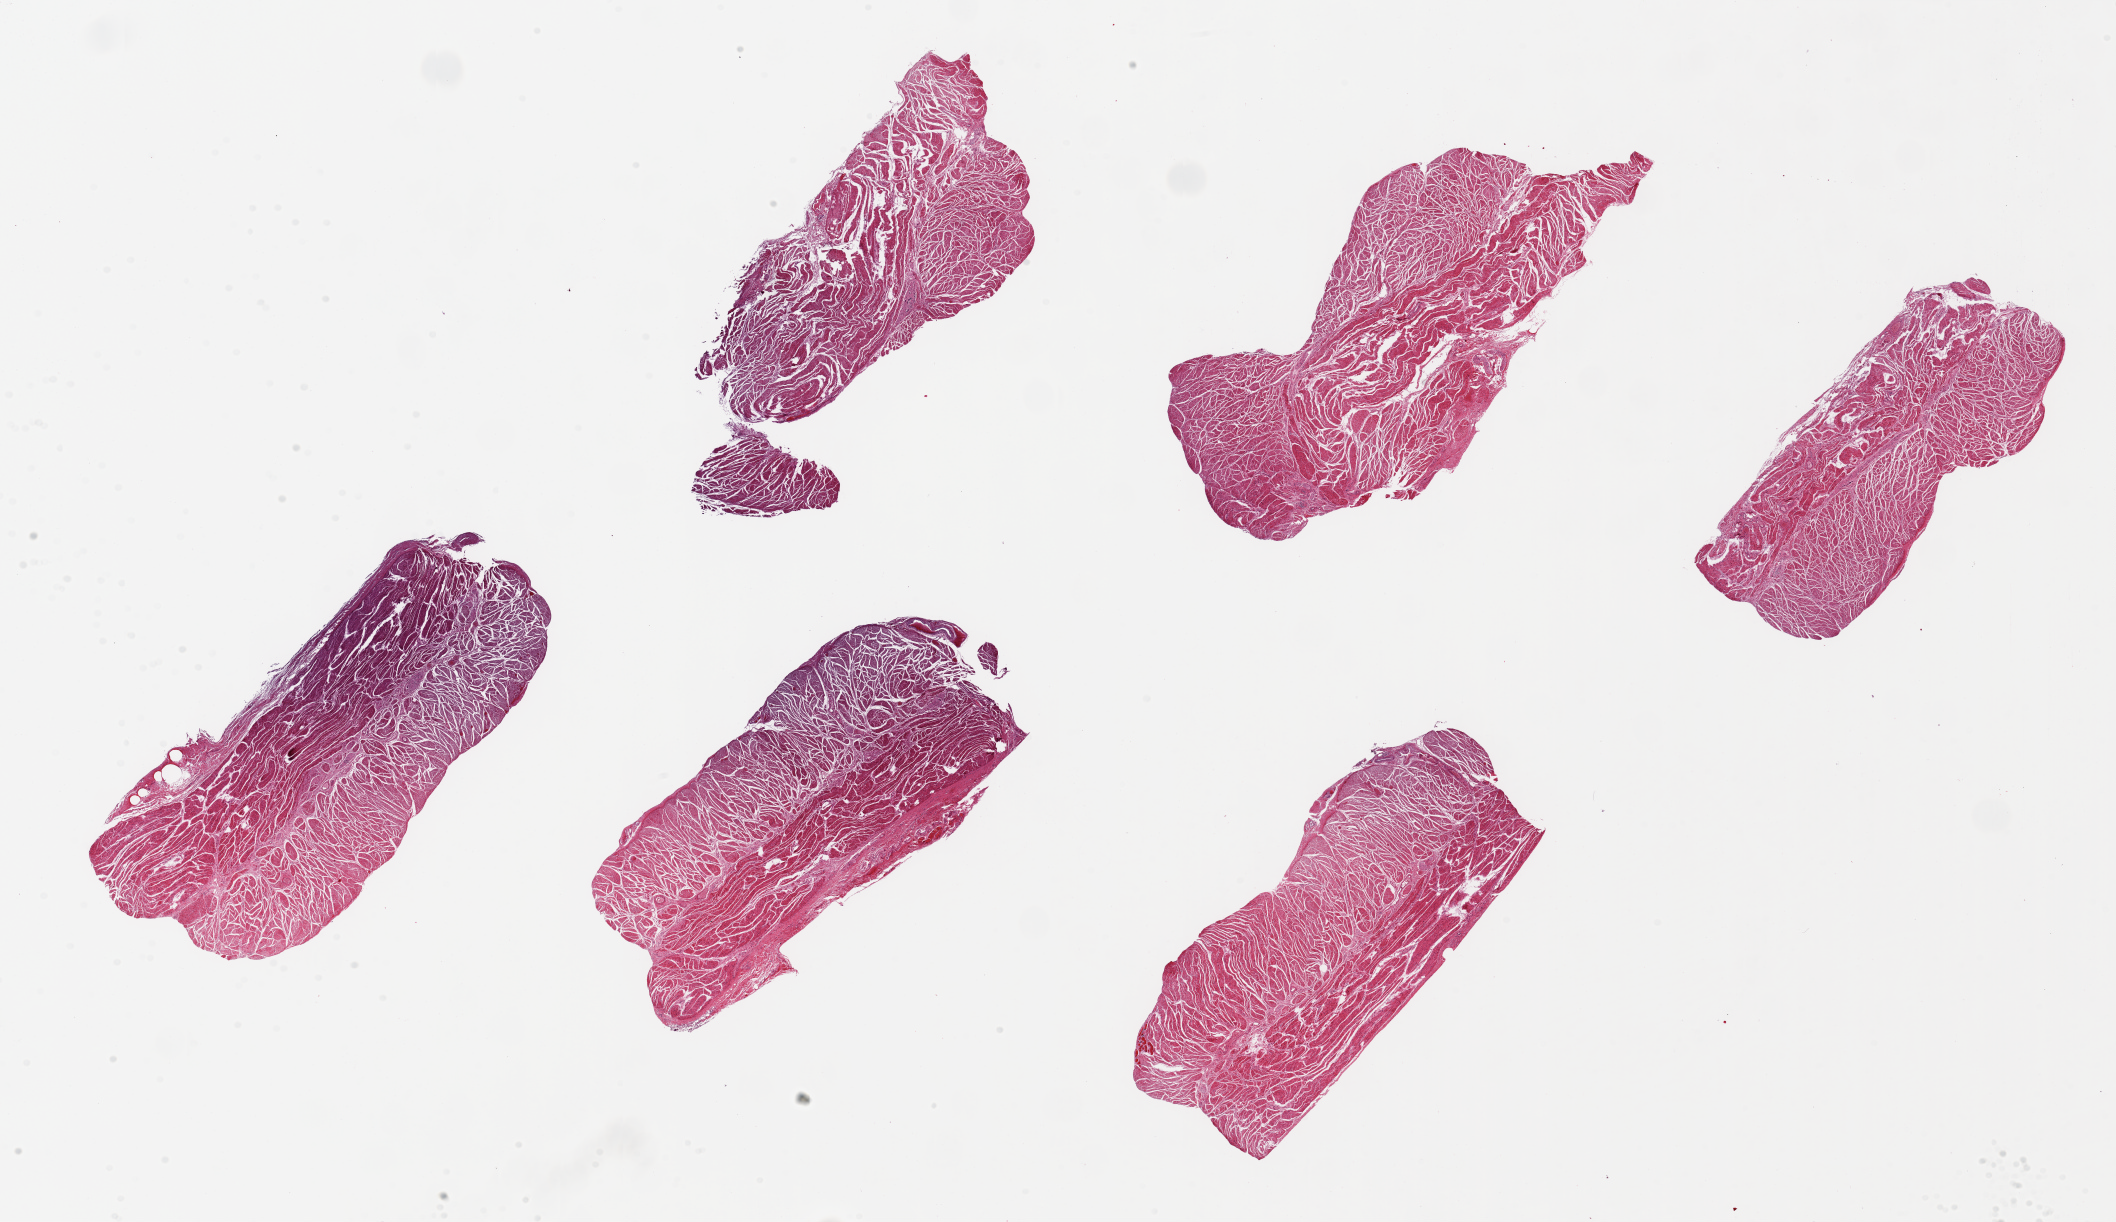
Haematoxylin and eosin whole-slide image — low-resolution overview of the scanned area, about 33.5 x 19.3 mm (acquisition: 20x scan), PAXgene-fixed paraffin-embedded (PFPE) section, sampled site (target tissue): gastroesophageal junction, donor tissue sample. Donor: female.
* pathologist's review note for this sample: 6 pieces ~ ~7x3mm, all muscle, clean specimens